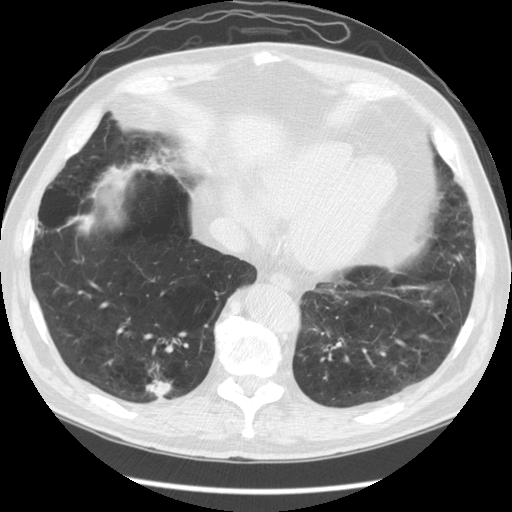
Low-dose screening chest CT, one axial slice. Slice 42 of 141 in the series (ordered by position). 120 kVp. Lung window (W 1500 / L -600 HU). 2.5 mm slice thickness. 512 × 512 image matrix.
Structures marked on this image (expert manual segmentation):
- lesion 1 (tumor, lower lobe of right lung): bounding box (x1, y1, x2, y2) in pixels: (146, 379, 172, 396)